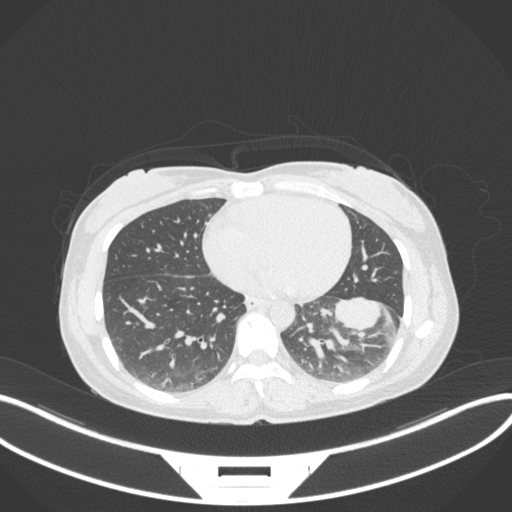
Chest CT, one axial slice. Position 137 of 361 along the scan axis. Reconstruction kernel B31f. 120 kVp. Lung window (W 1500 / L -600 HU). 1 mm slice thickness. 512 × 512 image matrix, field of view 400 × 400 mm. Patient: female, 41 years. From the clinical record (not read from this slice): clinical TNM (as recorded): T2a N3 M1b.
Structures marked on this image (rectangle marked by the reading radiologist):
- lung tumour (recorded histology: adenocarcinoma): bounding box <330,293,391,339> (left, top, right, bottom; pixels)